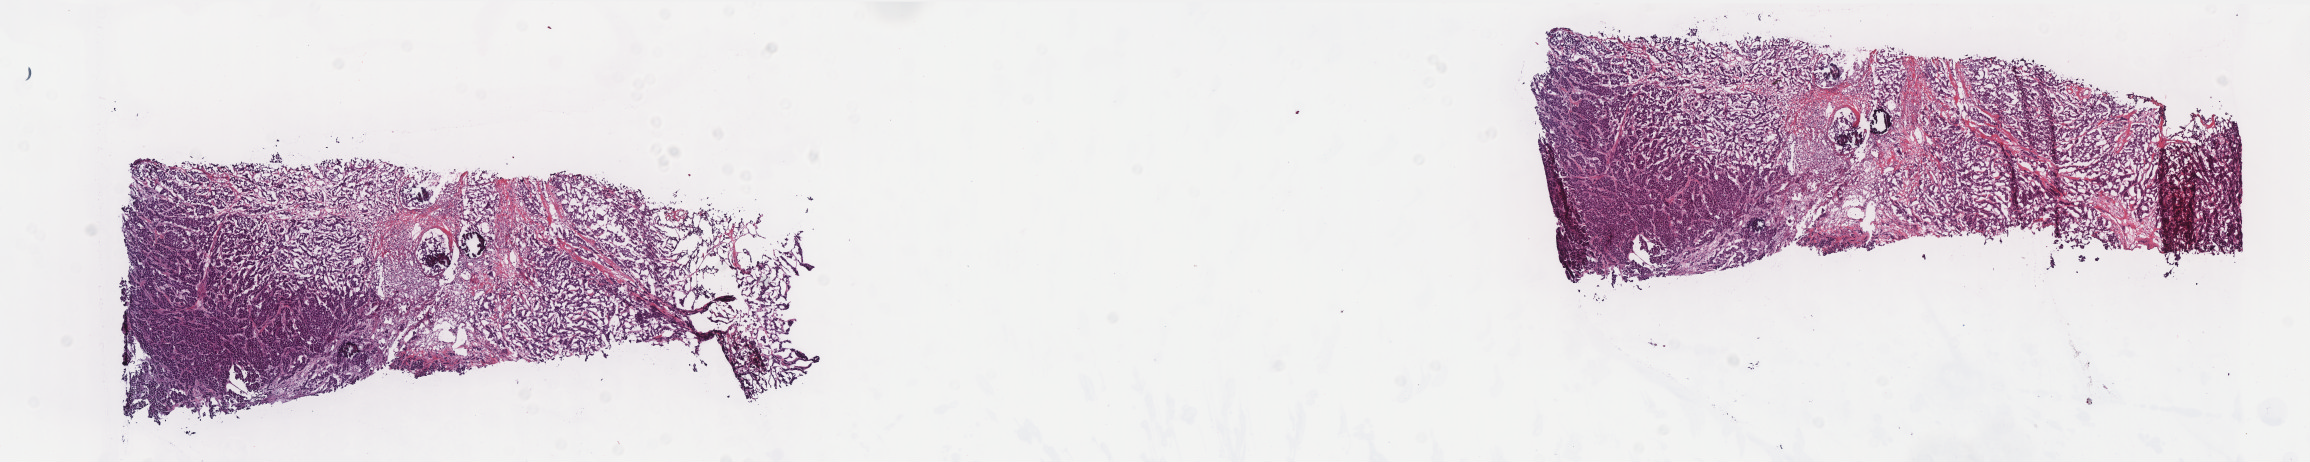
H&E-stained whole-slide image — a low-resolution overview of the entire scanned area, about 18.5 x 3.7 mm. Frozen section. Primary tumour sample from the breast. Patient: female, age at initial diagnosis 51 years. Slide review estimates, as recorded: tumour cells 80%, tumour nuclei 80%, normal cells 0%, stromal cells 19%, necrosis 1%. Inflammatory infiltration, as recorded: lymphocyte infiltration 4%, monocyte infiltration 15%, neutrophil infiltration 0%.
Pathologic diagnosis: Infiltrating duct carcinoma, NOS. Laterality: left. Lymph nodes positive (case pathology): 2 of 15 examined. AJCC pathologic stage: IIB.